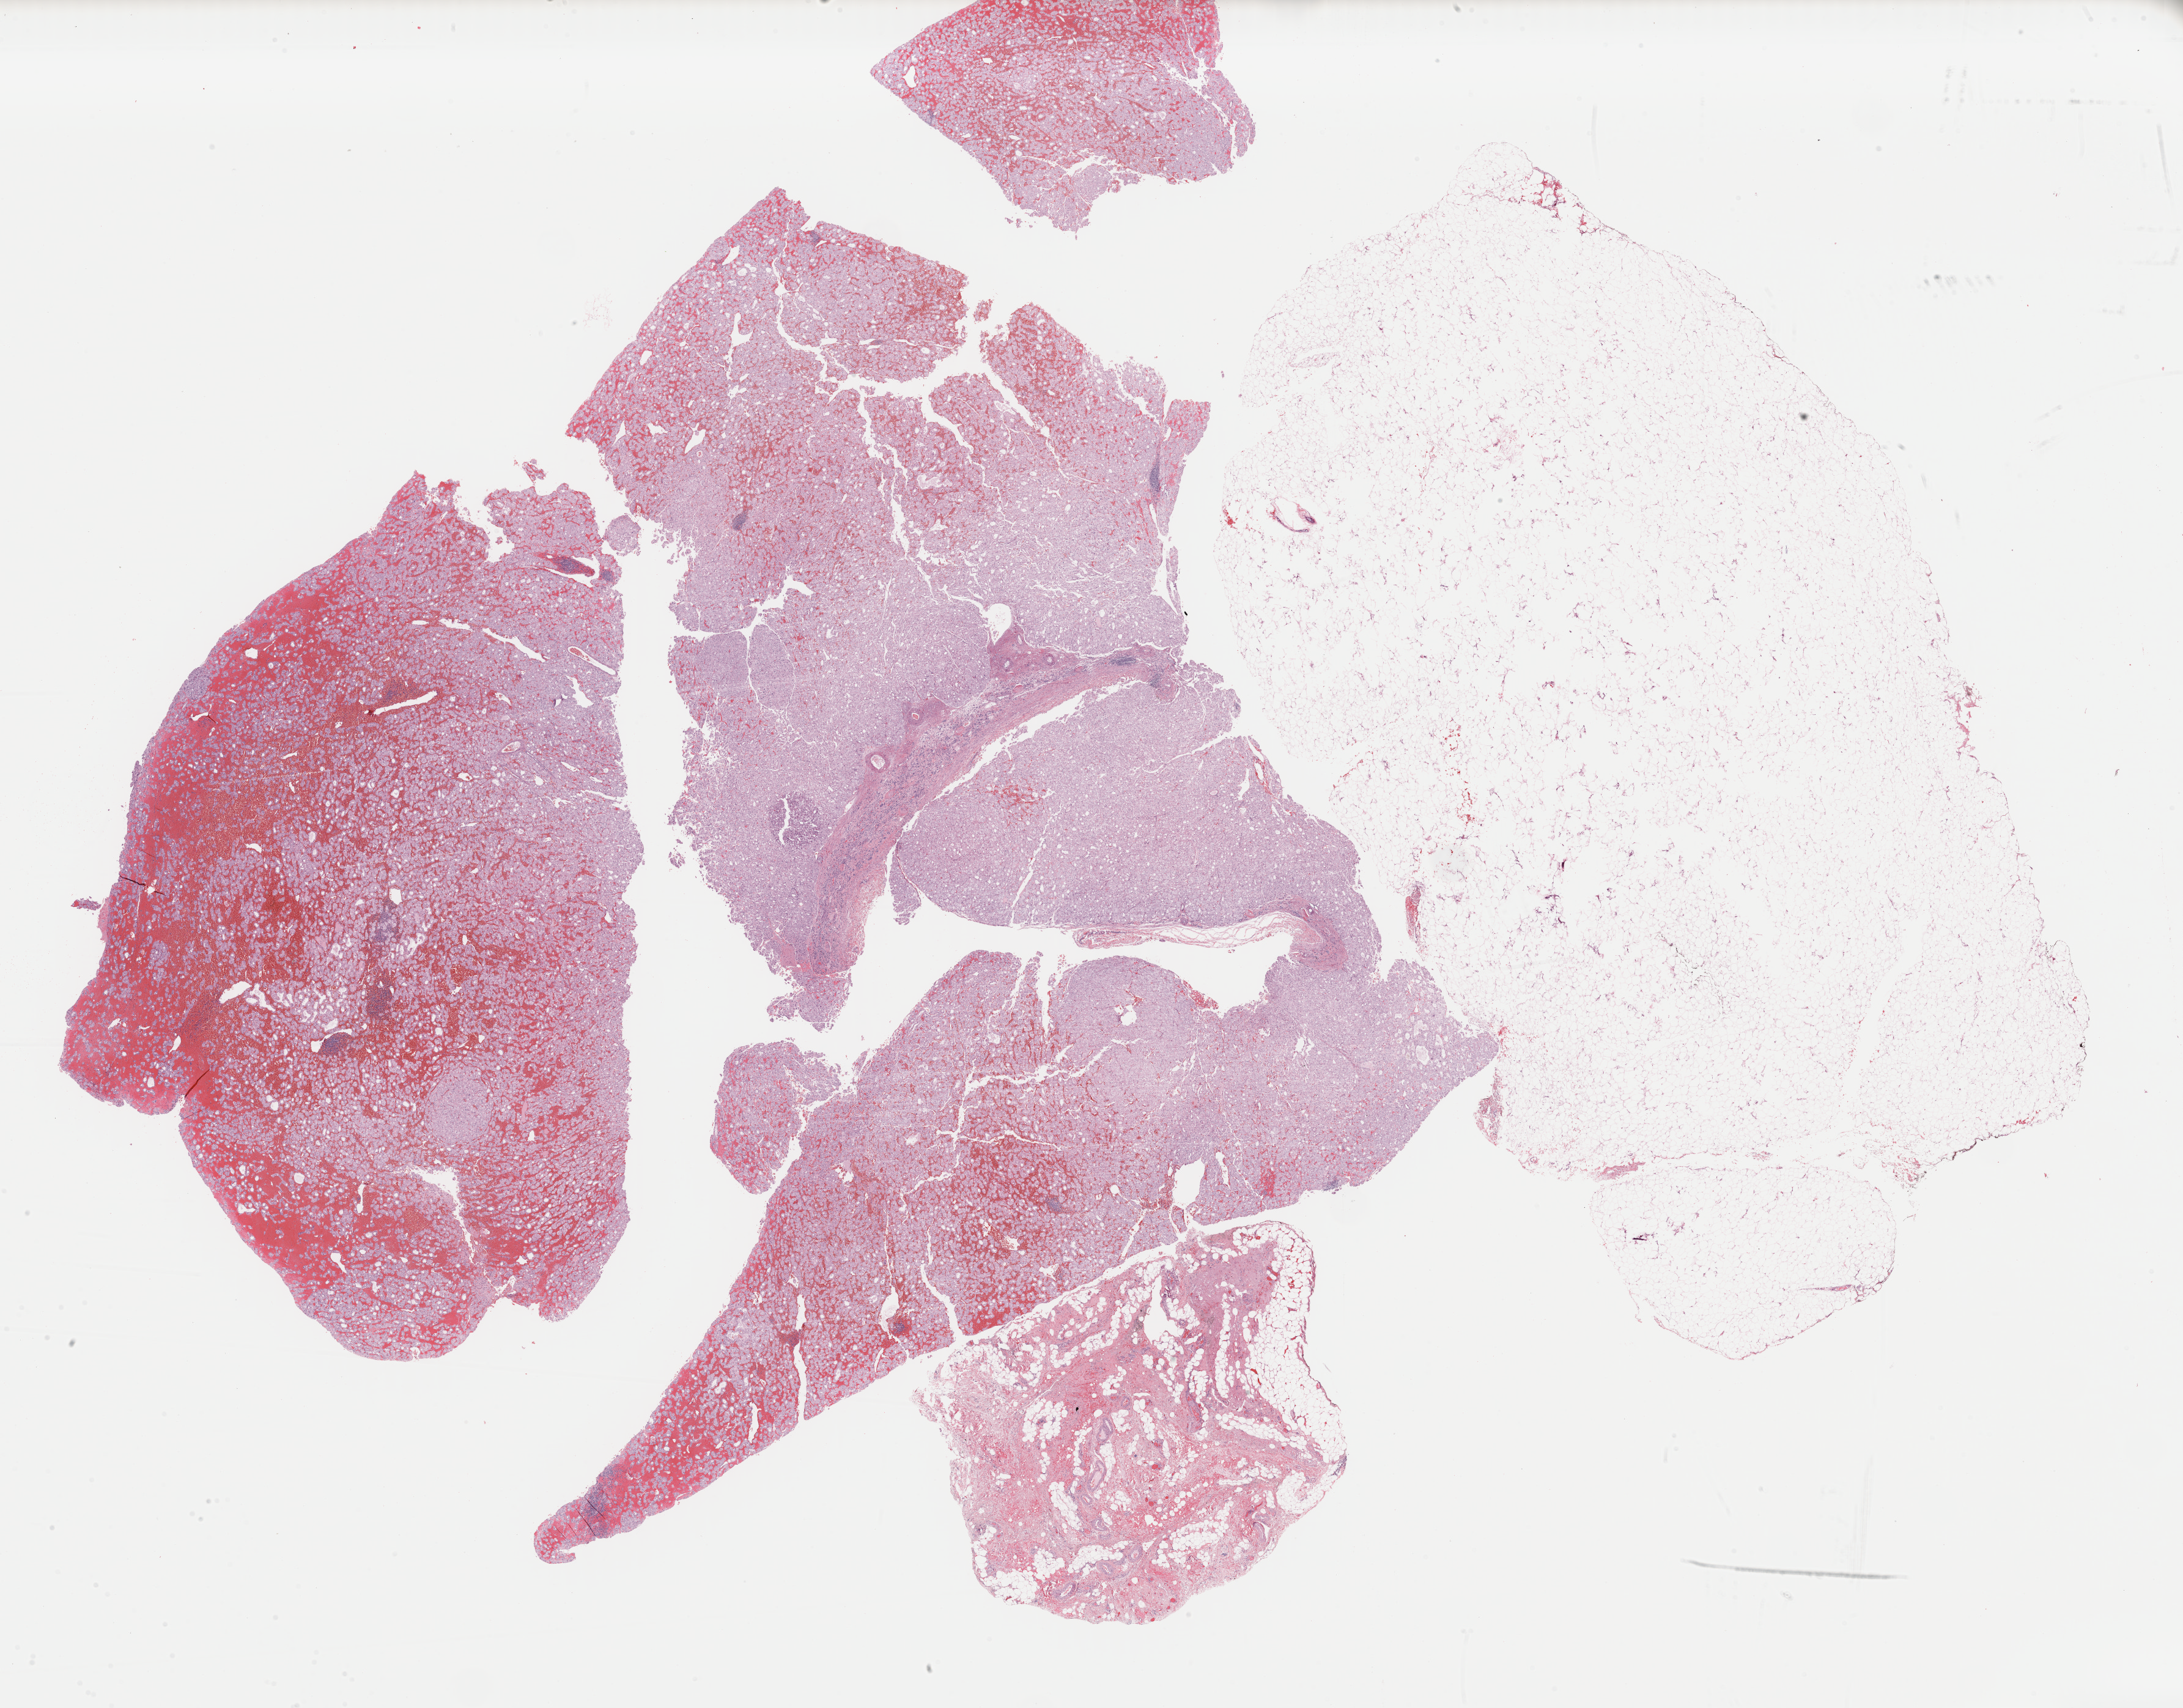
Hematoxylin and eosin (H&E) stained whole-slide image, low-resolution overview of the scanned area, about 28.2 x 22.0 mm (slide scanned at 40x), FFPE section, kidney, primary tumour sample. Female patient; age at initial diagnosis 74 years.
Diagnosis: Renal cell carcinoma, chromophobe type. Lymph nodes positive (case pathology): 0 of 1 examined. AJCC pathologic stage: I (7th edition).